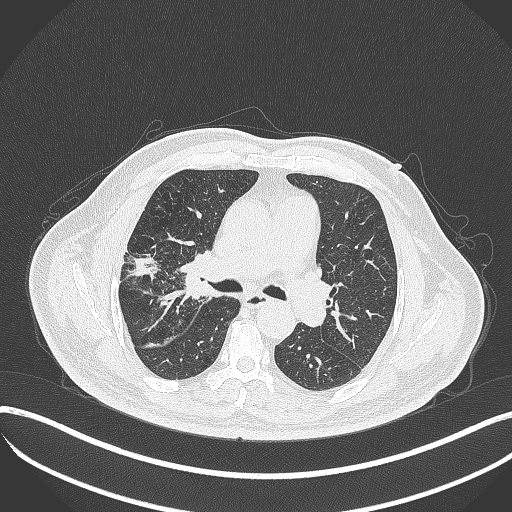
Chest CT, one axial slice. Position 218 of 401 along the scan axis. 120 kVp. Lung window (W 1500 / L -600 HU). 1 mm slice thickness. 512 × 512 image matrix, field of view 400 × 400 mm. Patient: male, 72 years. Case-level facts recorded for this patient, not image findings: clinical TNM (as recorded): T1c N0 M0; histopathological grade: G2.
Outlined on this slice (rectangle marked by the reading radiologist):
- lung tumour (recorded histology: squamous cell carcinoma): bounding box [x1, y1, x2, y2] px = [169, 246, 203, 306]